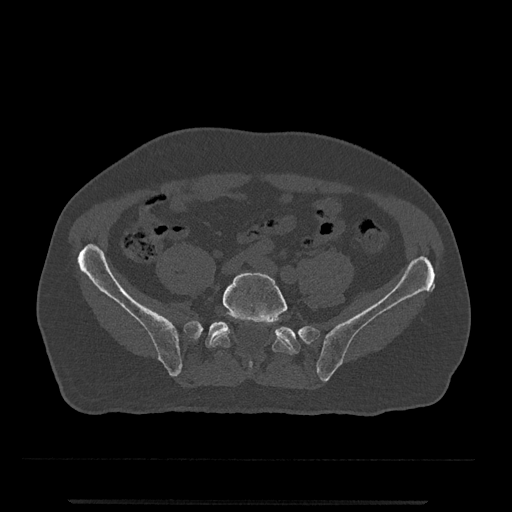
CT including the spine, one axial slice; position 51 of 797 along the scan axis; 120 kVp; bone window (W 1800 / L 400 HU); 0.5 mm slice thickness; 512 × 512 image matrix, field of view 419 × 419 mm. Male patient, age 63 years. Case-level facts recorded for this patient, not image findings: primary cancer: prostate.
Structures marked on this image (semi-automatic segmentation, software-assisted and operator-edited):
- L5 vertebra: box from (x=210, y=272) to (x=292, y=370) px